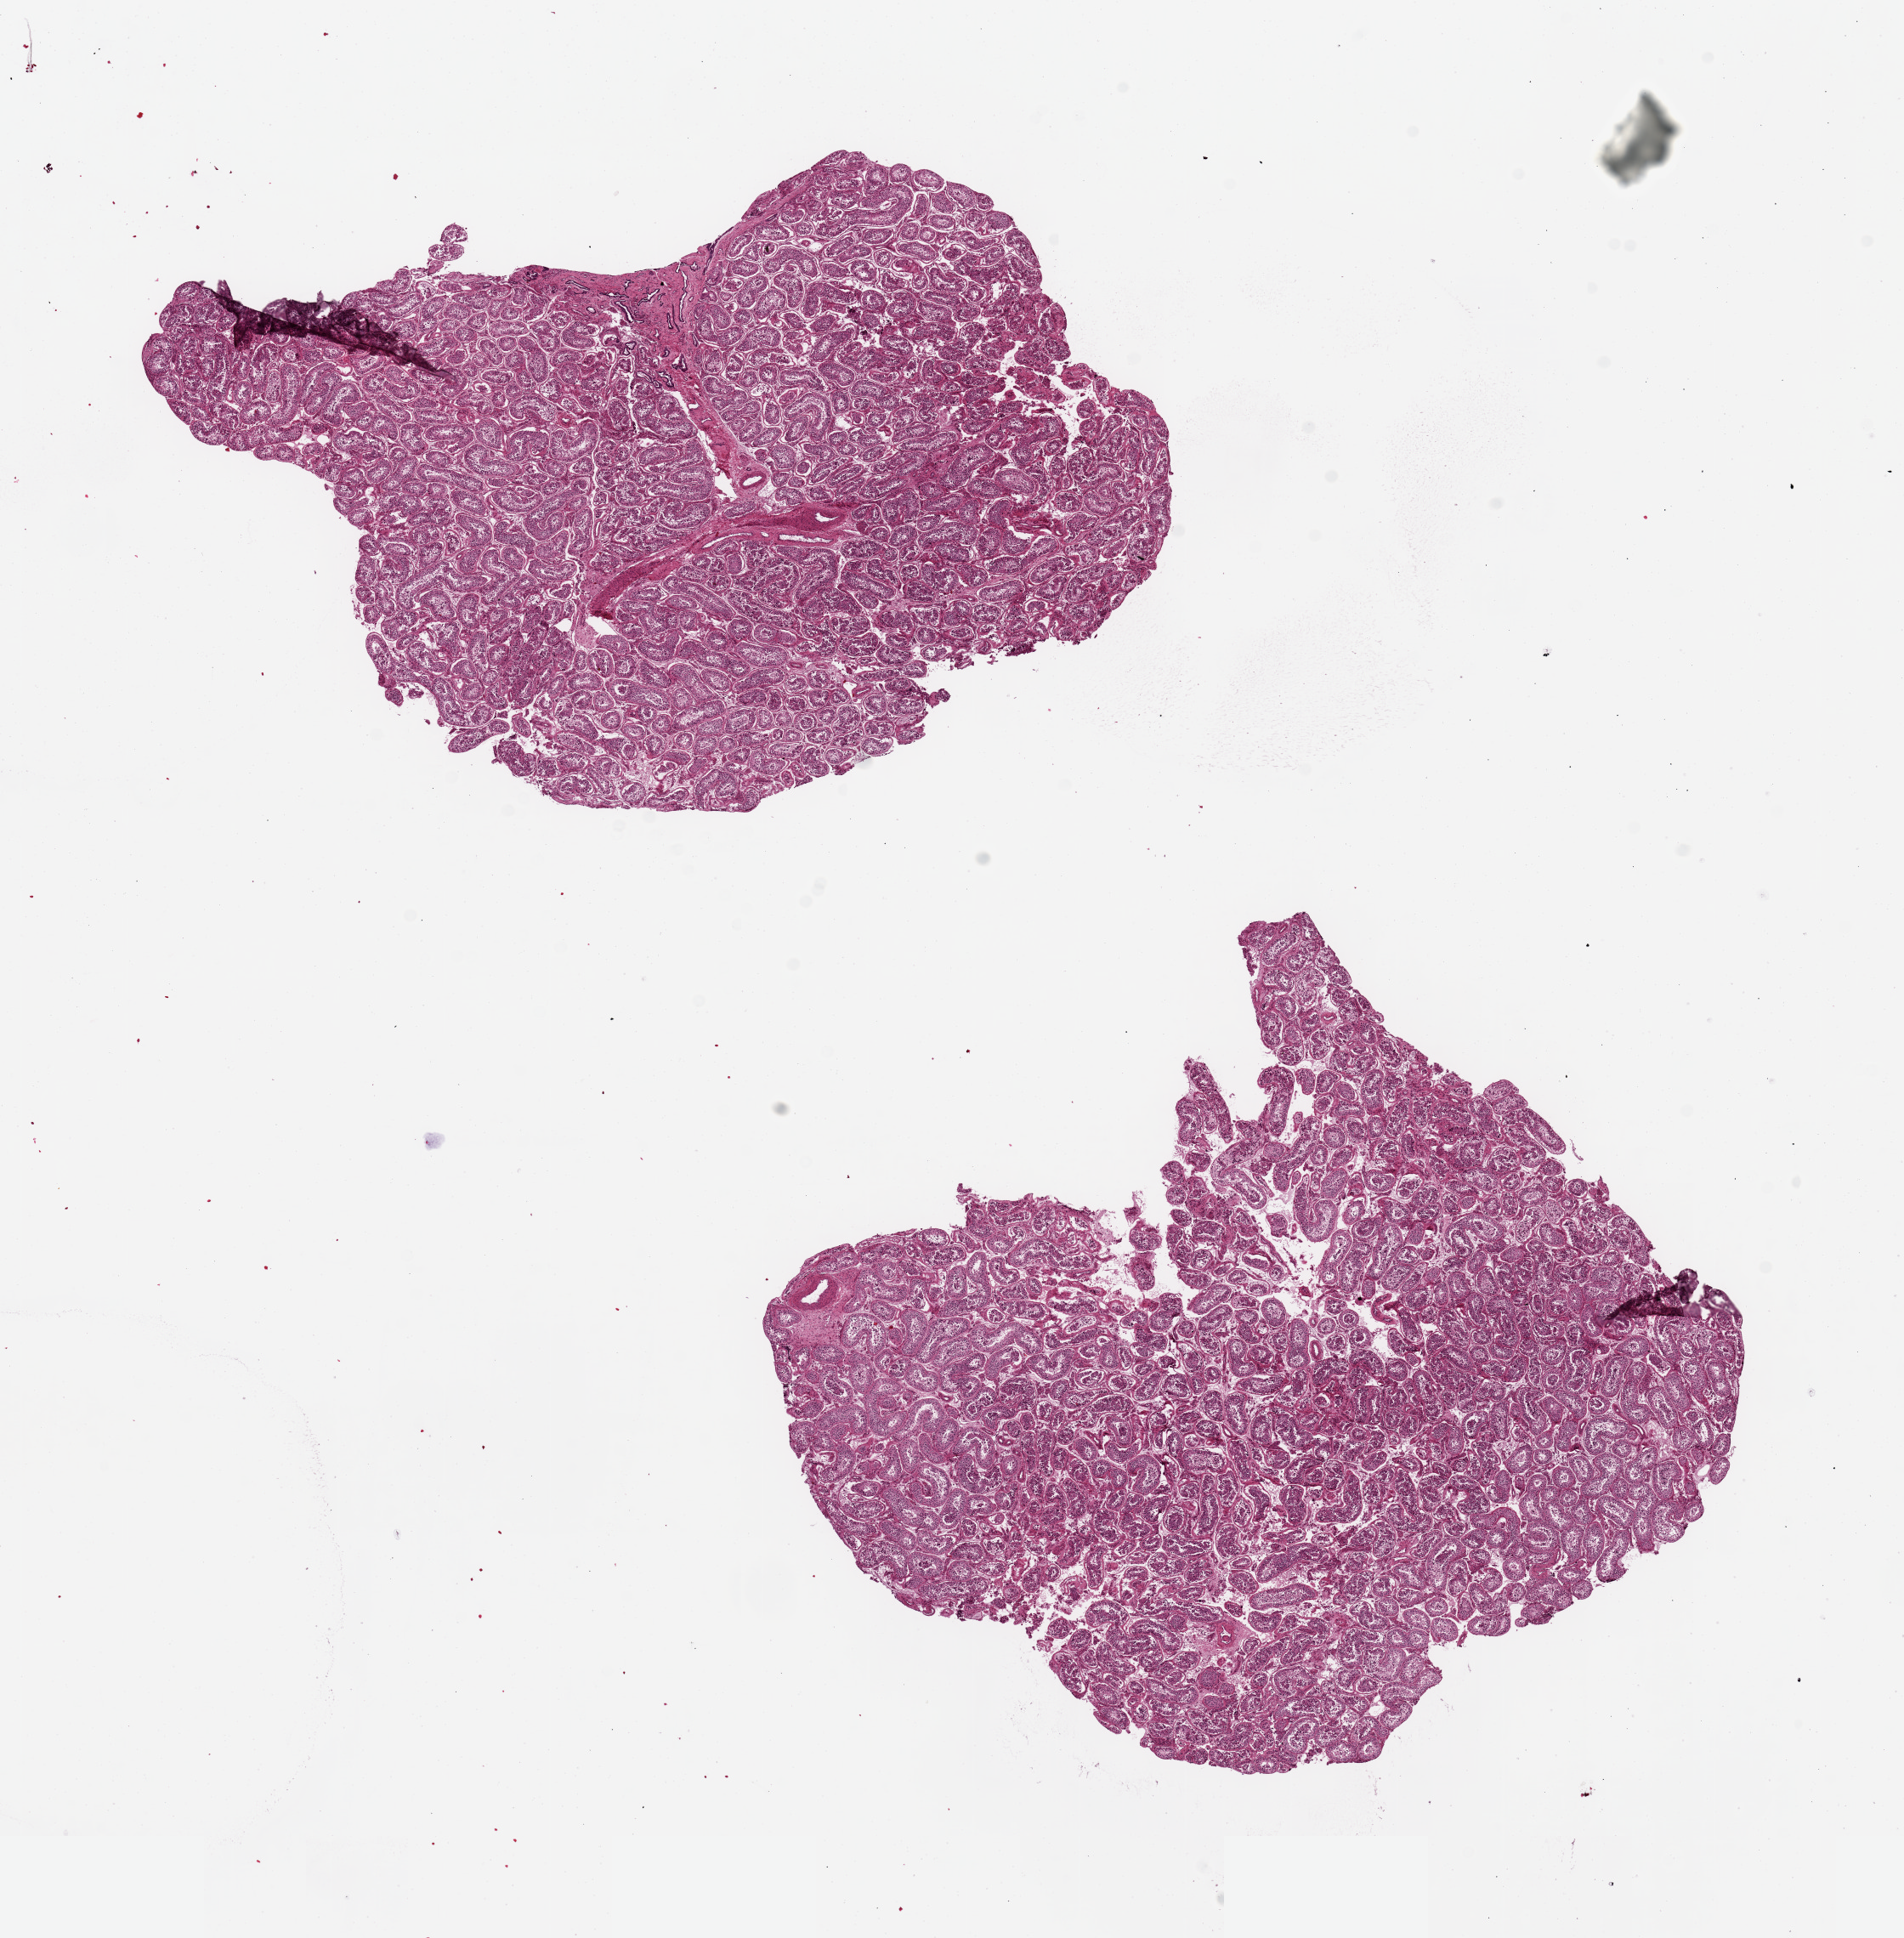
Whole-slide image, H&E stain — a low-resolution overview of the entire scanned area, about 17.7 x 18.0 mm (slide scanned at 20x), PAXgene-fixed paraffin-embedded (PFPE) section, section of testis (target tissue), donor tissue sample. Donor sex: male.
Reviewer comment on this tissue sample: 2 pieces /`9x6mm, spermatogenesis is present.